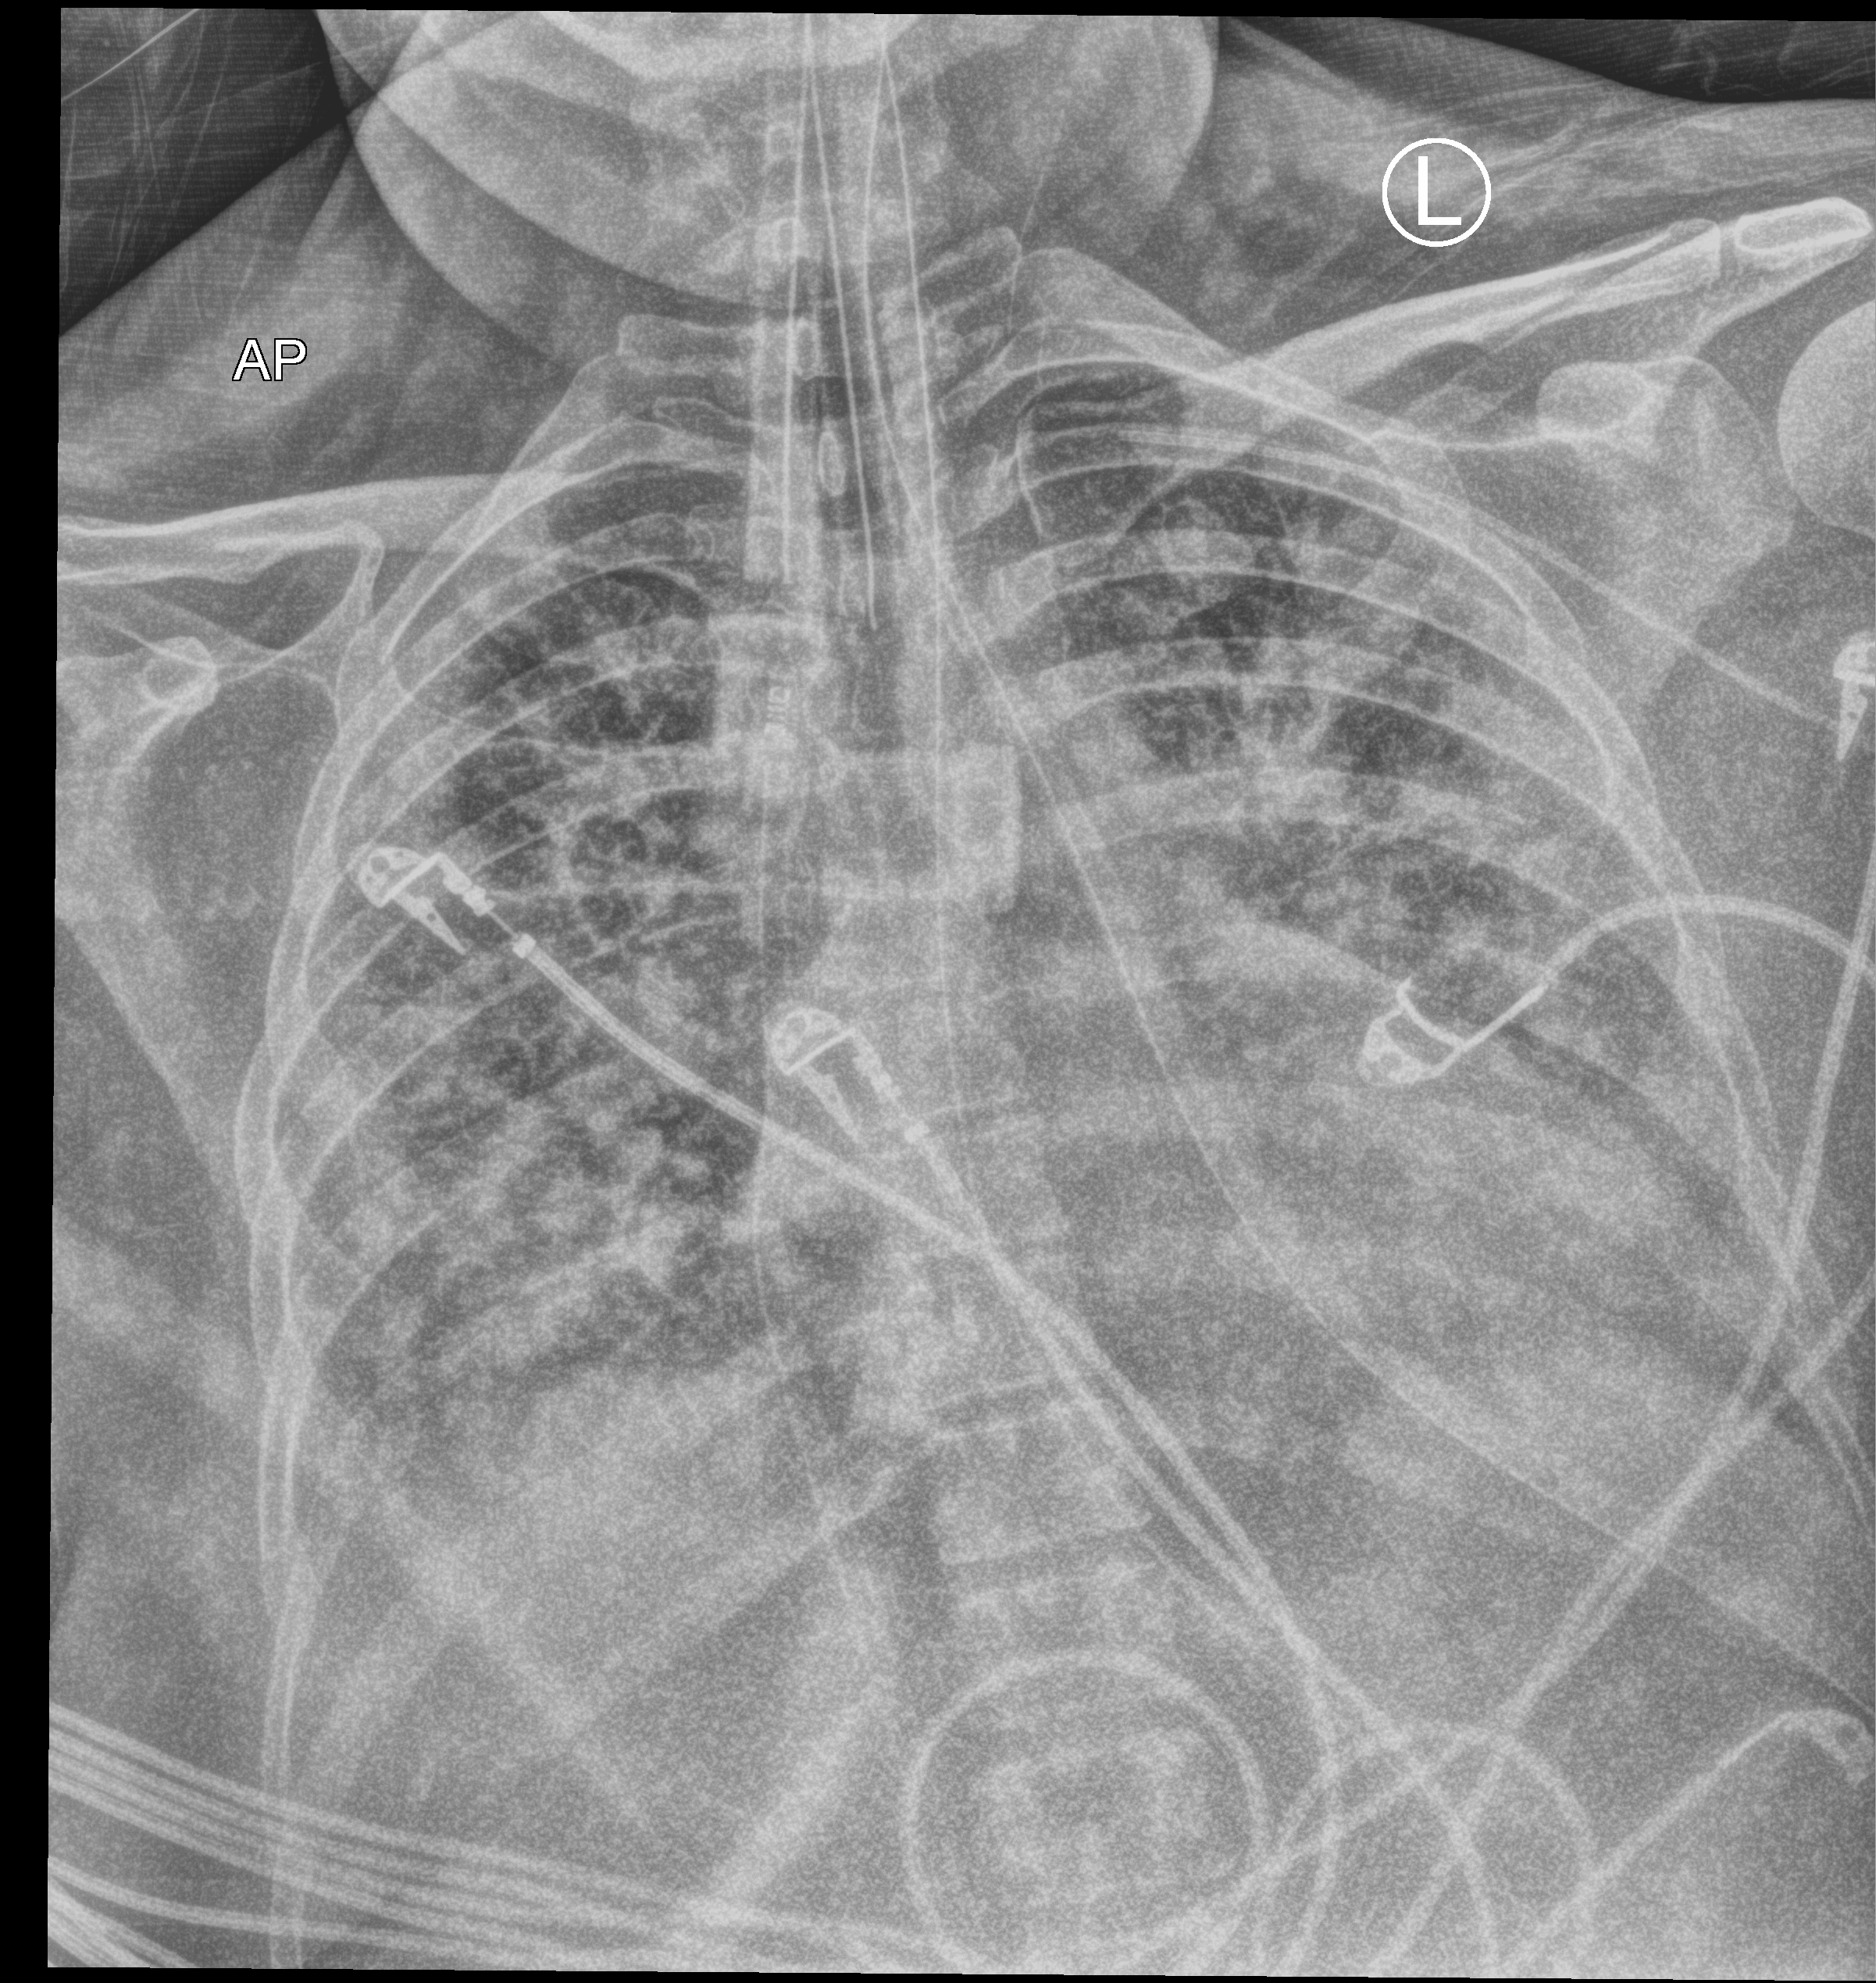
Bedside chest radiograph (computed radiography), anteroposterior (AP) projection. Patient hospitalised with COVID-19; female, aged 18–59 years.
Hospital-stay facts (about this admission, not read from this image; timing relative to this image not recorded): mechanically ventilated during this hospital stay: yes.